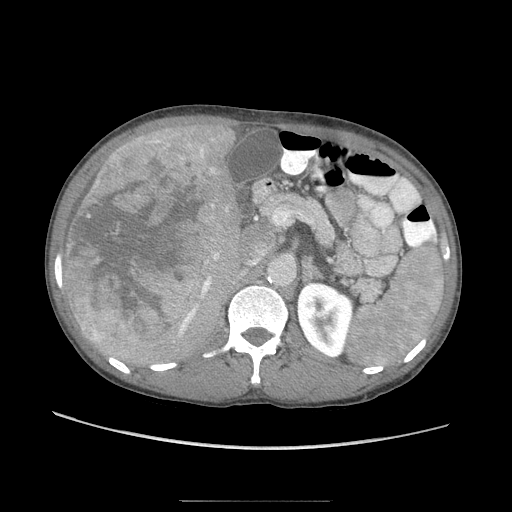
Contrast-enhanced abdominal CT (liver protocol), one axial slice. Slice 45 of 103 in the series (ordered by position). 120 kVp. Soft-tissue window (W 400 / L 40 HU). 512 × 512 image matrix, field of view 380 × 380 mm. From the clinical record (not read from this slice): diagnosis: hepatocellular carcinoma (patient treated with transarterial chemoembolisation; whether this scan precedes or follows treatment is not stated here); TNM stage (as recorded): Stage-IIIA.
Outlined on this slice (semi-automatic segmentation, software-assisted and operator-edited):
- liver parenchyma outside the tumour (the mass and vessels are separate outlines, so this box may not span the whole liver): bounding box <66,118,248,370> (left, top, right, bottom; pixels)
- mass: <62,128,220,347>
- liver vessels: <204,158,223,252>